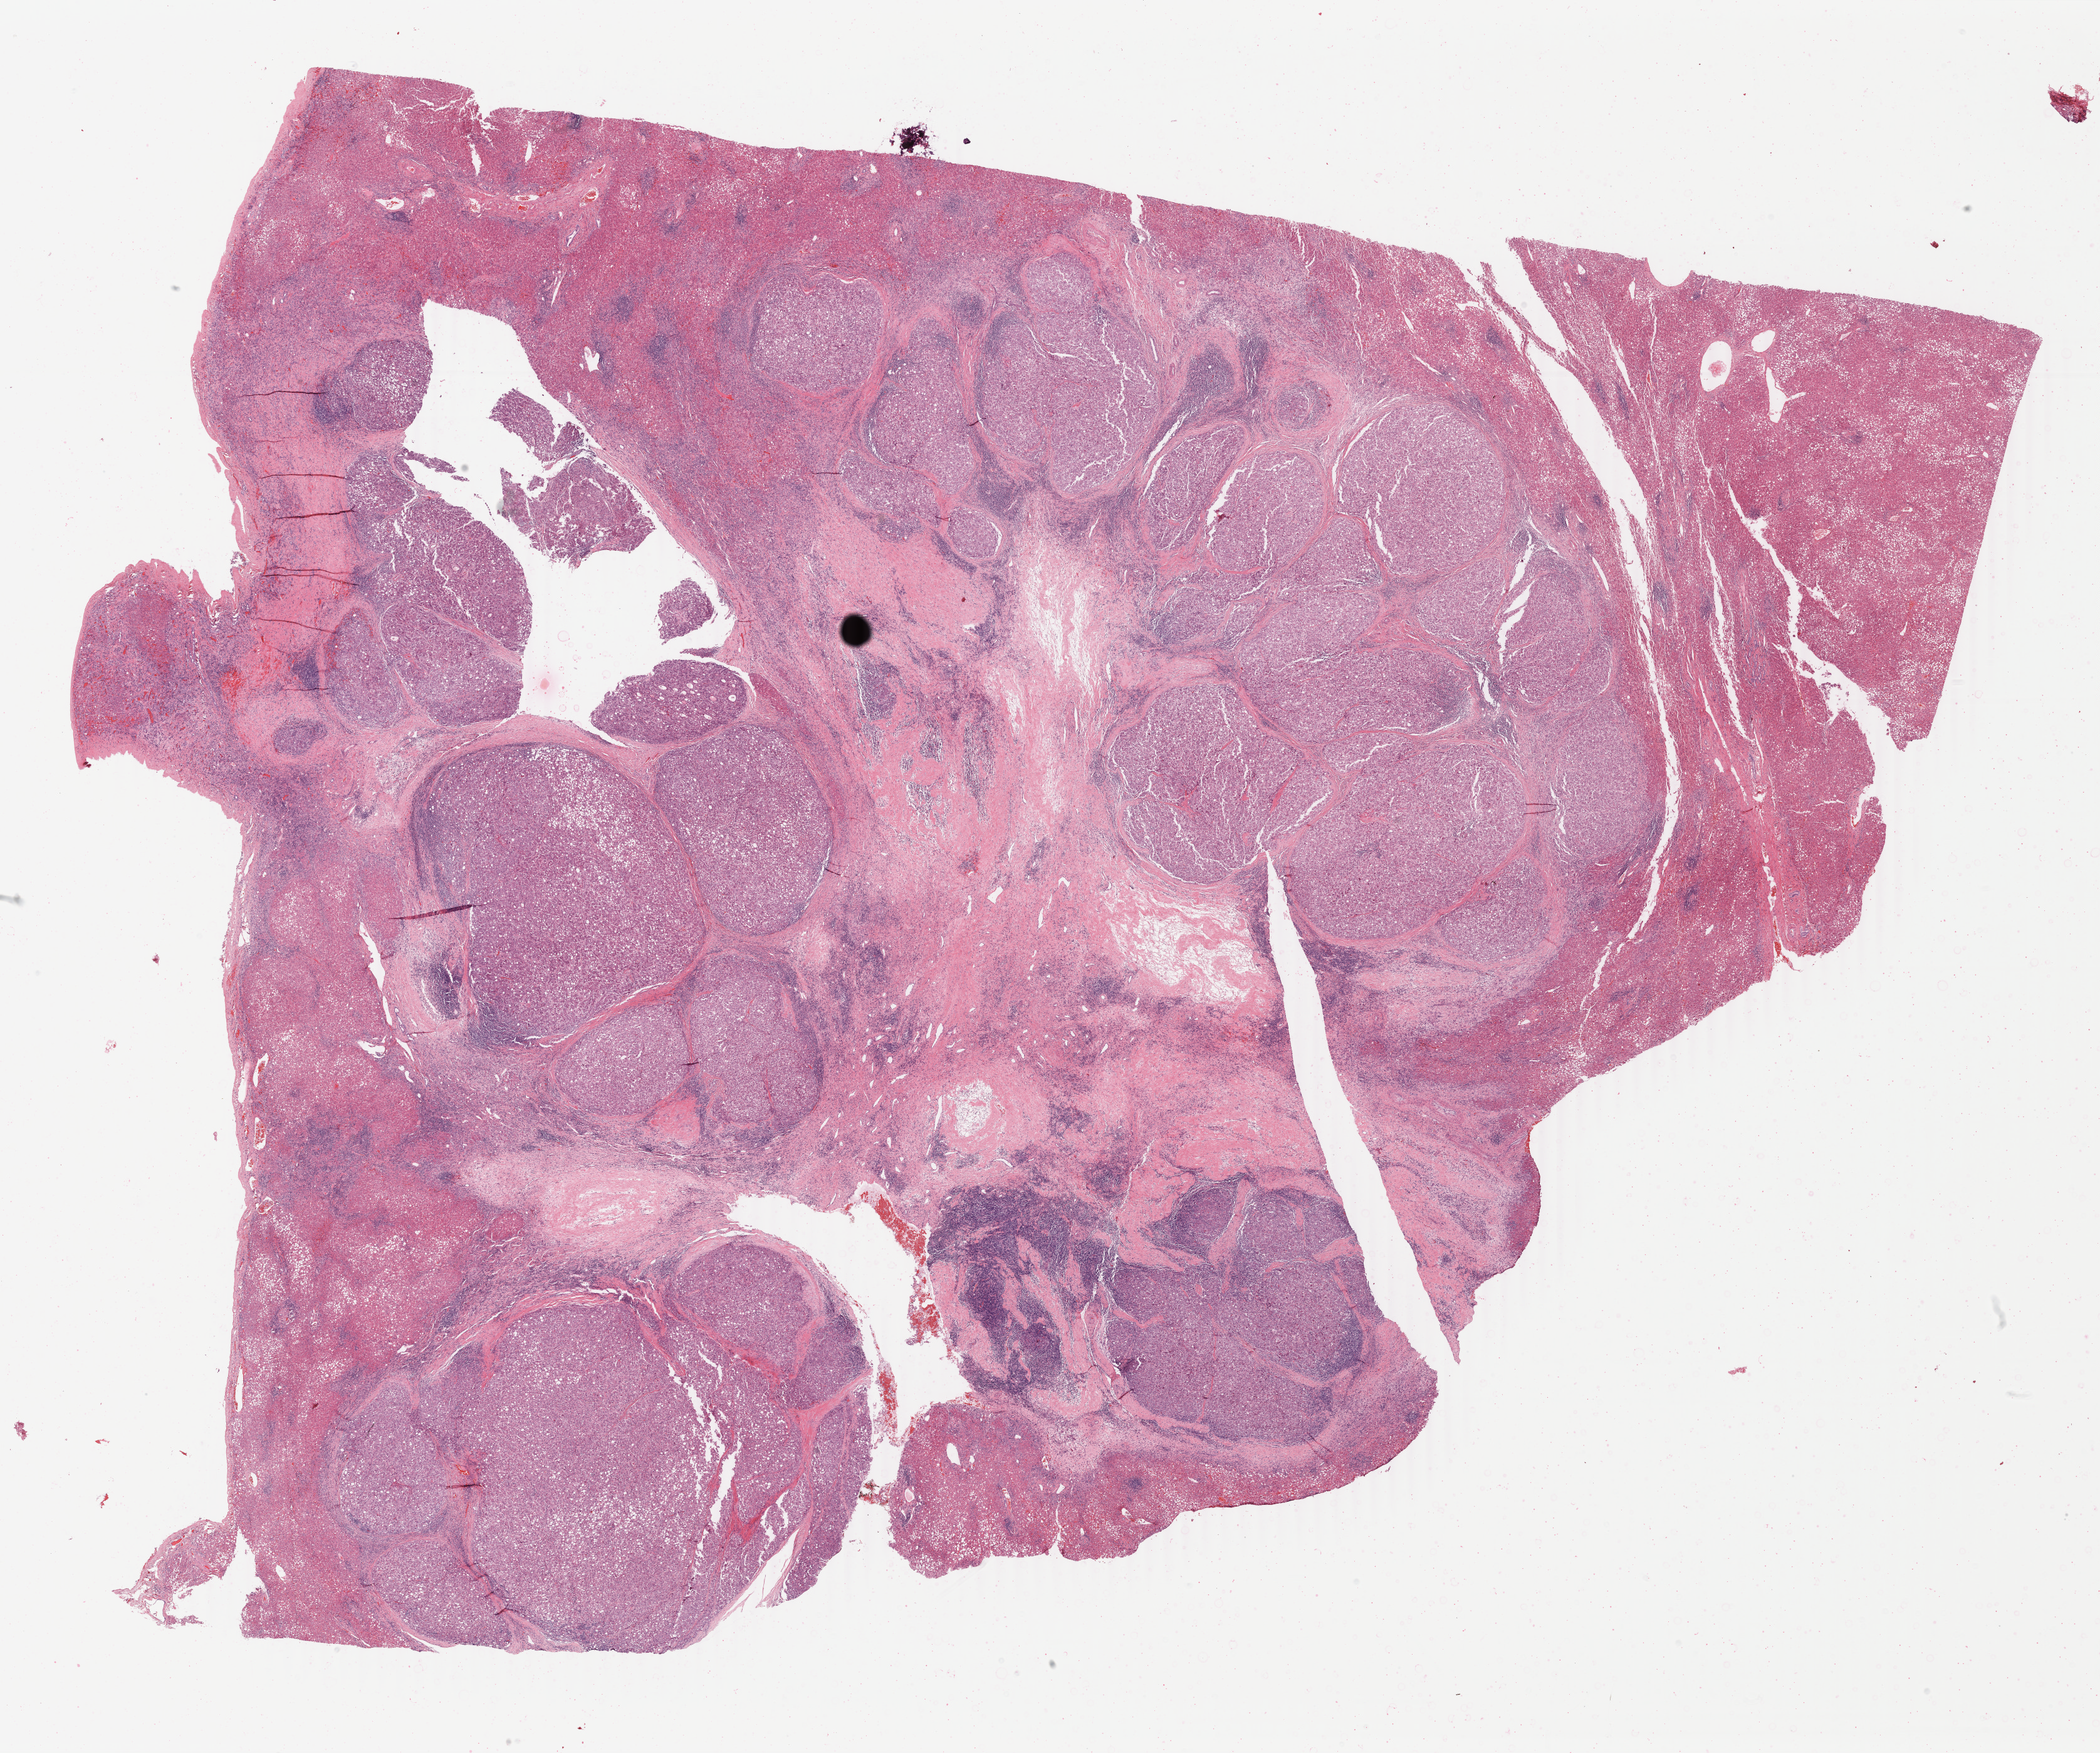
Whole-slide histology image, Hematoxylin and eosin (H&E) stained — shown as a low-resolution overview of the whole scanned area (about 26.7 x 22.3 mm, from a 40x scan); FFPE section; primary tumour sample from the liver. Patient: male, age at initial diagnosis 66 years. Histologic grade: G2 (moderately differentiated).
* AJCC pathologic stage: I (7th edition)
* pathologic diagnosis: Hepatocellular carcinoma, NOS